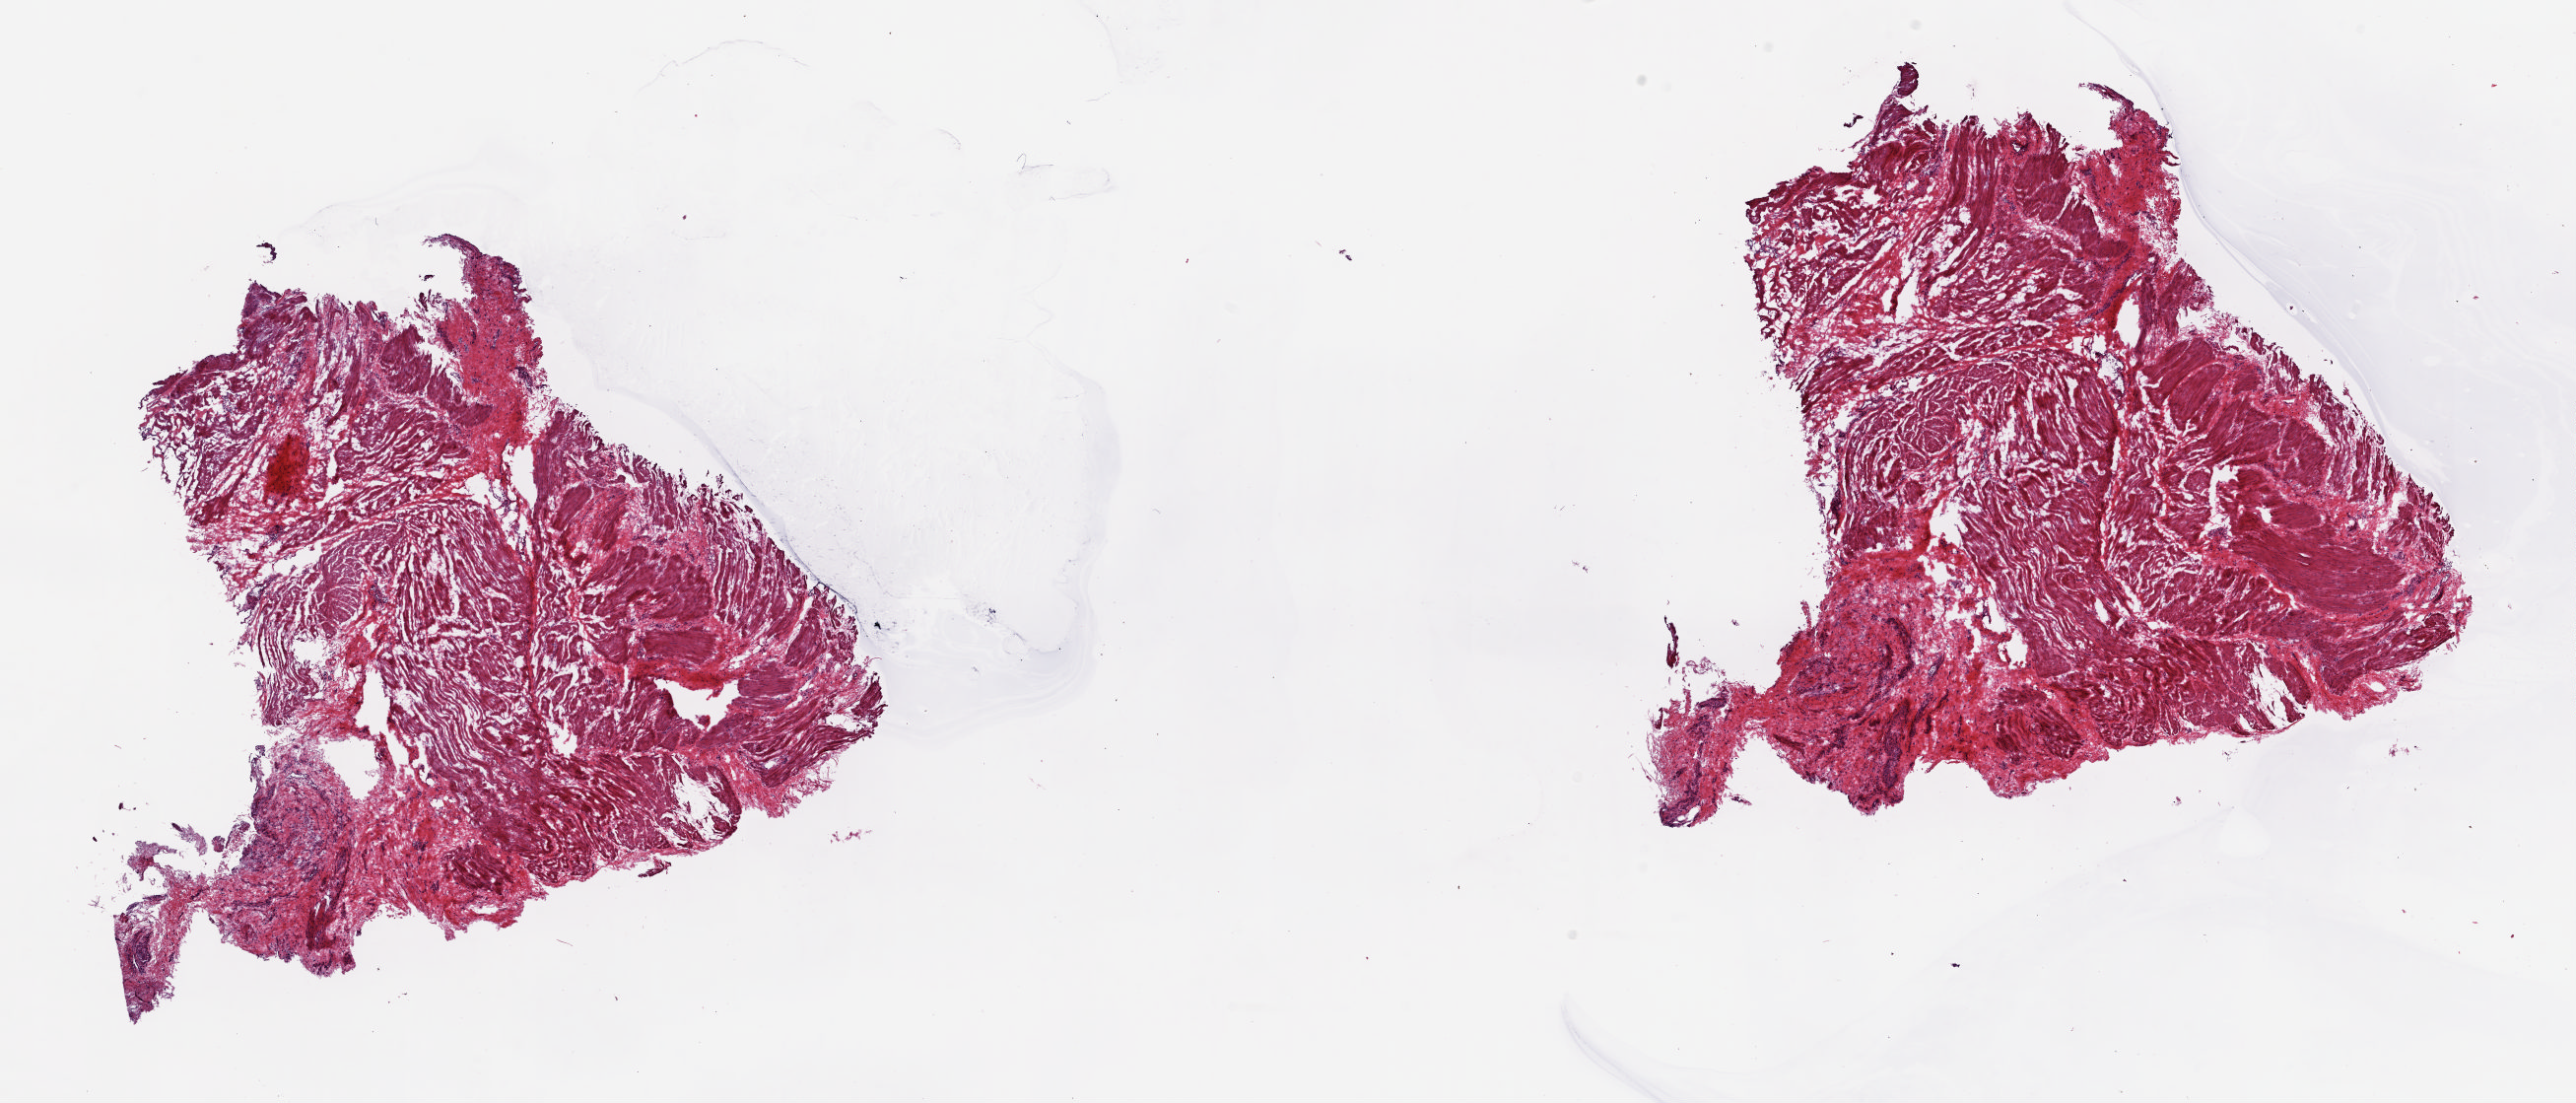
Whole-slide histology image, Hematoxylin and eosin (H&E) stained — shown as a low-resolution overview of the whole scanned area (about 20.8 x 8.9 mm, from a 20x scan), frozen section from the top of the tissue portion, bladder, solid tissue normal (non-tumour tissue) sample. Male, age 72 years at initial diagnosis. Slide review estimates, as recorded: tumour cells 0%, tumour nuclei 0%, normal cells 0%, stromal cells 100%, necrosis 0%. Infiltration values recorded for this section: lymphocyte infiltration 5%, monocyte infiltration 0%, neutrophil infiltration 0%.
• this section: solid tissue normal sample (biorepository sample class)
• patient diagnosis: Transitional cell carcinoma (trigone of bladder)